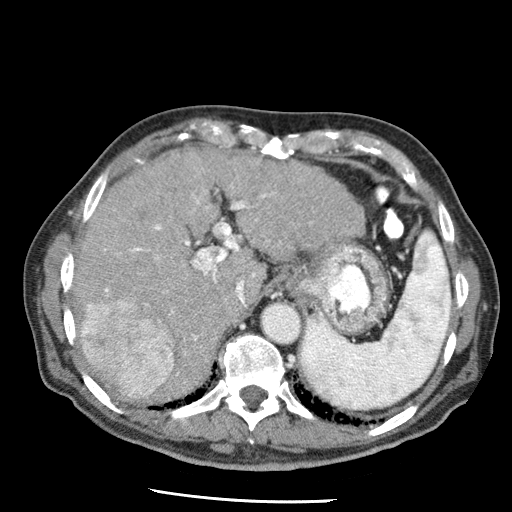
Contrast-enhanced abdominal CT (liver protocol), one axial slice; slice 46 of 79 in the series (ordered by position); 120 kVp; soft-tissue window (W 400 / L 40 HU); 2.5 mm slice thickness; 512 × 512 image matrix, field of view 320 × 320 mm. From the clinical record (not read from this slice): diagnosis: hepatocellular carcinoma (patient treated with transarterial chemoembolisation; whether this scan precedes or follows treatment is not stated here); TNM stage (as recorded): Stage-IIIA; Child-Pugh class: A; tumour nodularity: multinodular; tumour size: 7 cm.
Outlined on this slice (semi-automatically segmented with operator editing):
- liver parenchyma outside the tumour (the mass and vessels are separate outlines, so this box may not span the whole liver): bounding box [x1, y1, x2, y2] px = [72, 148, 366, 398]
- mass: [80, 300, 174, 398]
- liver vessels: [105, 184, 274, 375]